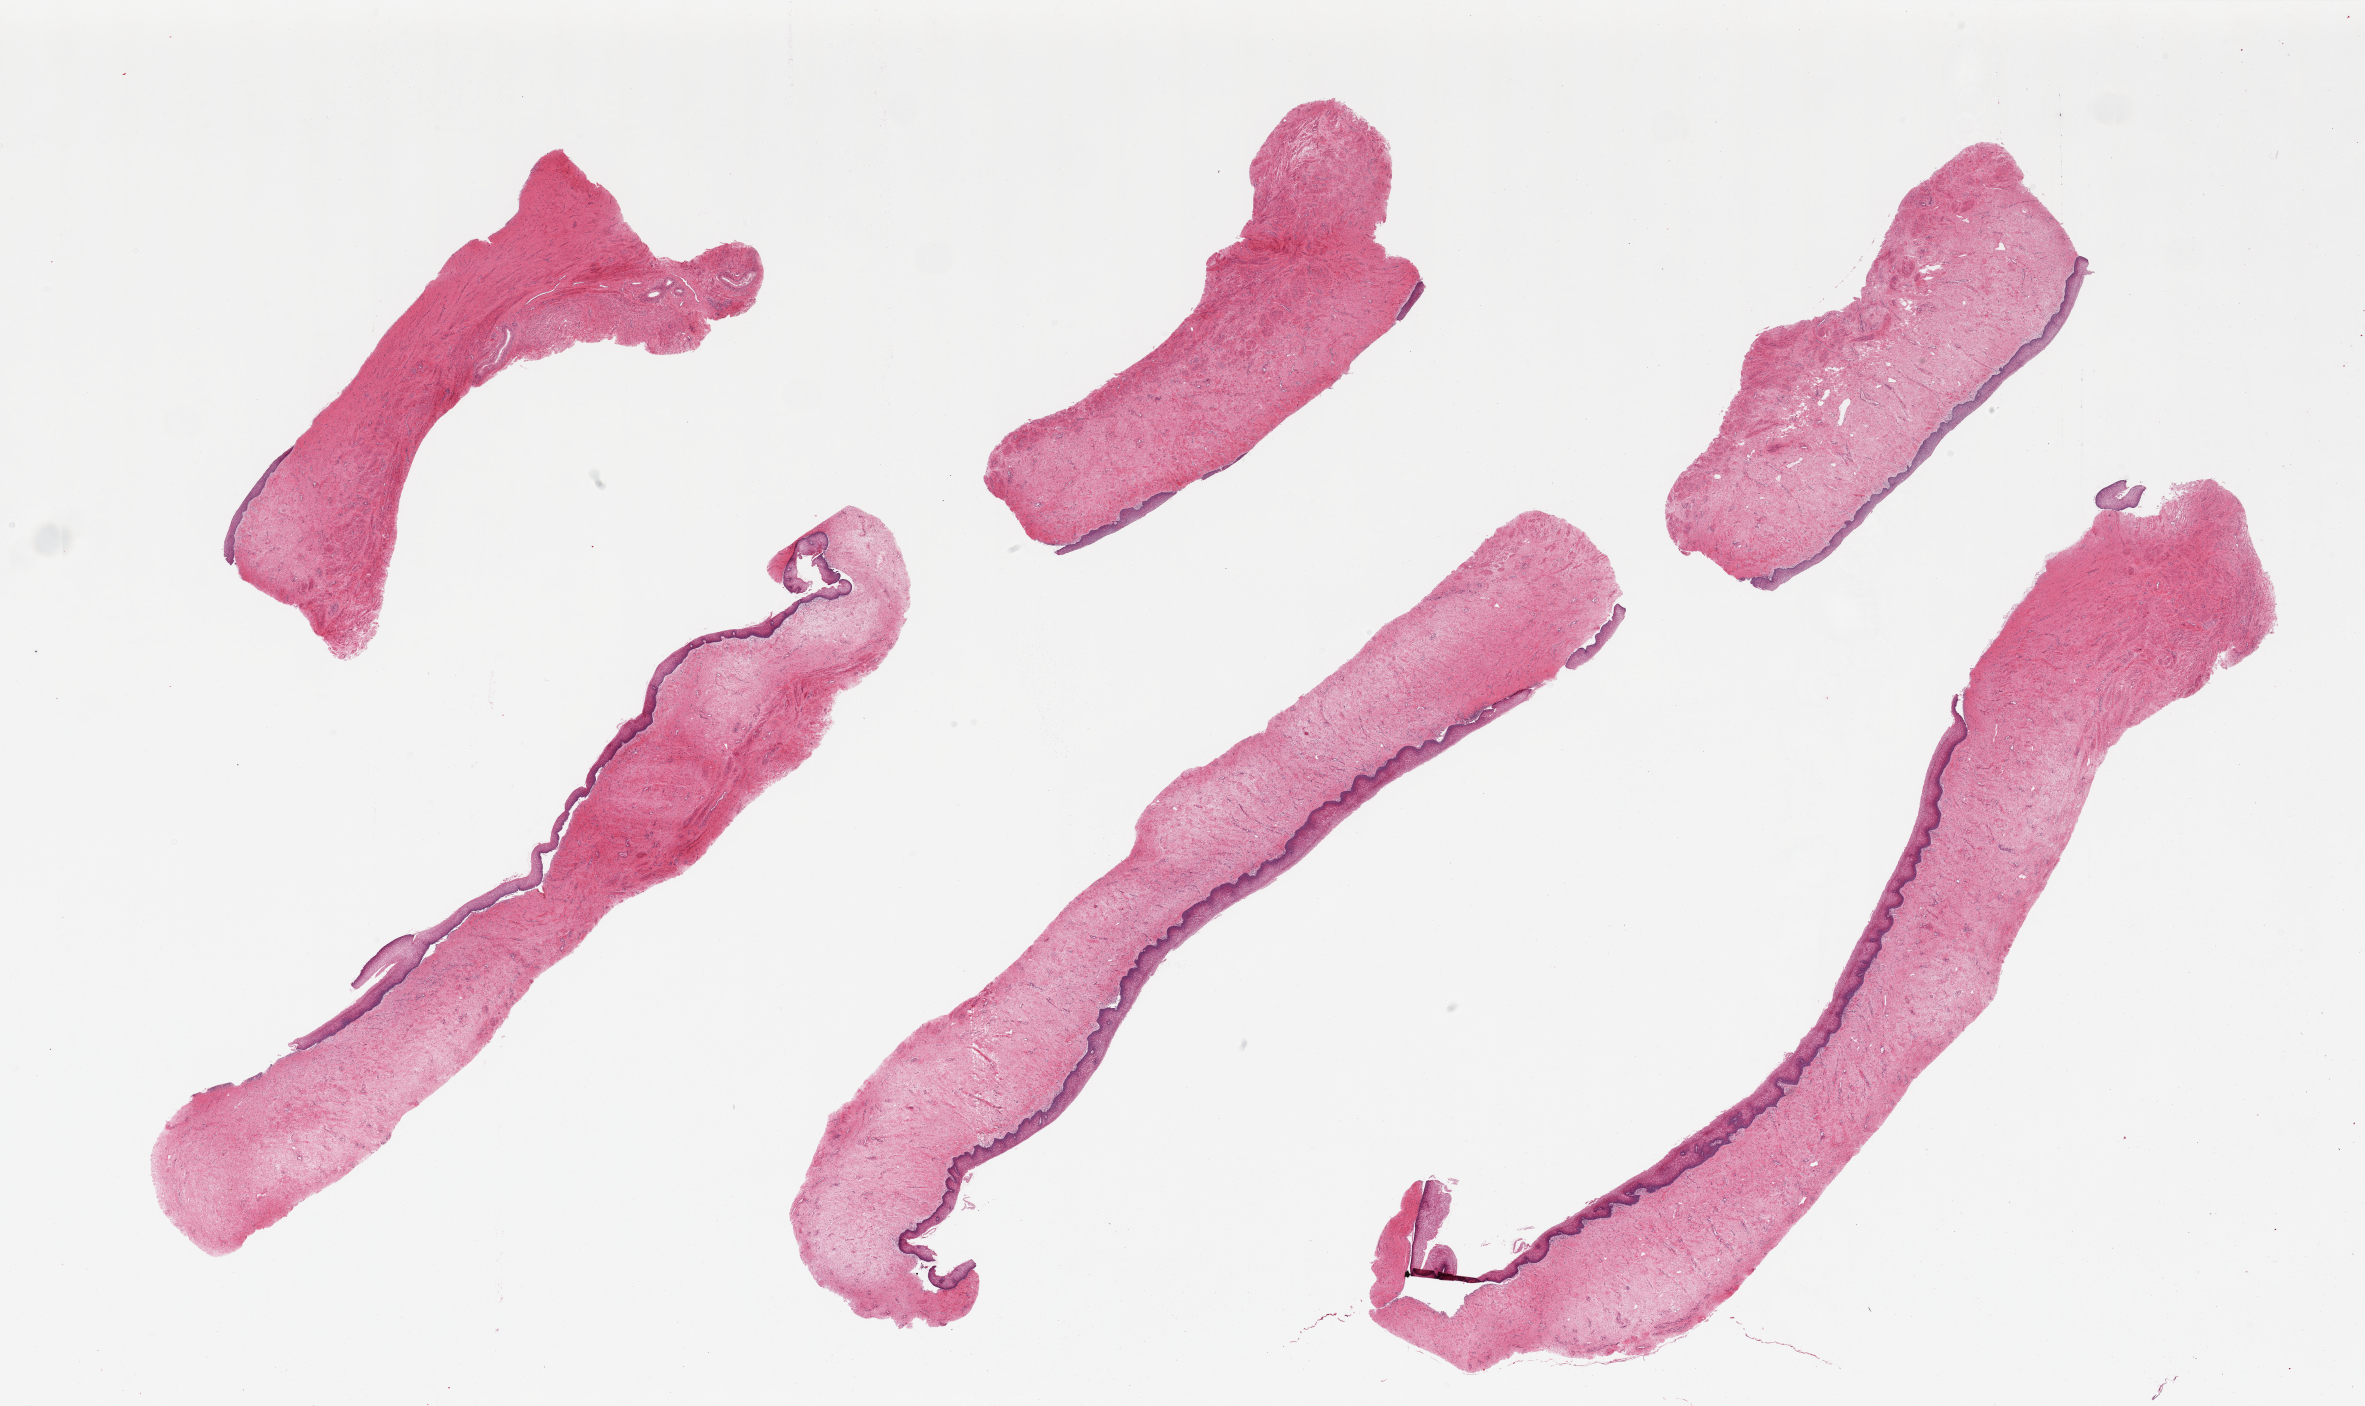
Hematoxylin and eosin (H&E) whole-slide image — whole scanned area (about 37.4 x 22.2 mm, from a 20x scan) shown as a low-resolution overview, PAXgene-fixed, paraffin-embedded tissue, section of vagina (target tissue), tissue donor sample. Donor: female.
Review note (as recorded): 6 pieces.